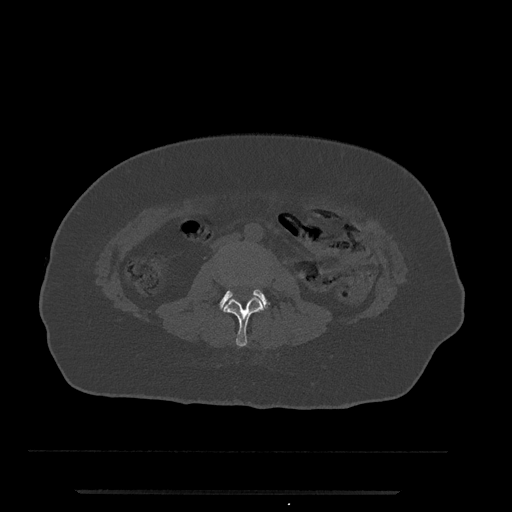
CT including the spine, one axial slice. Slice 5 of 797 in the series (ordered by position). Reconstruction kernel Br40s/3. Bone window (W 1800 / L 400 HU). 0.5 mm slice thickness. 512 × 512 image matrix, field of view 440 × 440 mm. Female patient, age 51 years. Case-level facts recorded for this patient, not image findings: primary cancer: neuro; vertebrae with lytic lesions (as recorded): T8.
Annotated regions visible in this slice (semi-automatic segmentation, software-assisted and operator-edited):
- L2 vertebra: box from (x=223, y=282) to (x=264, y=347) px